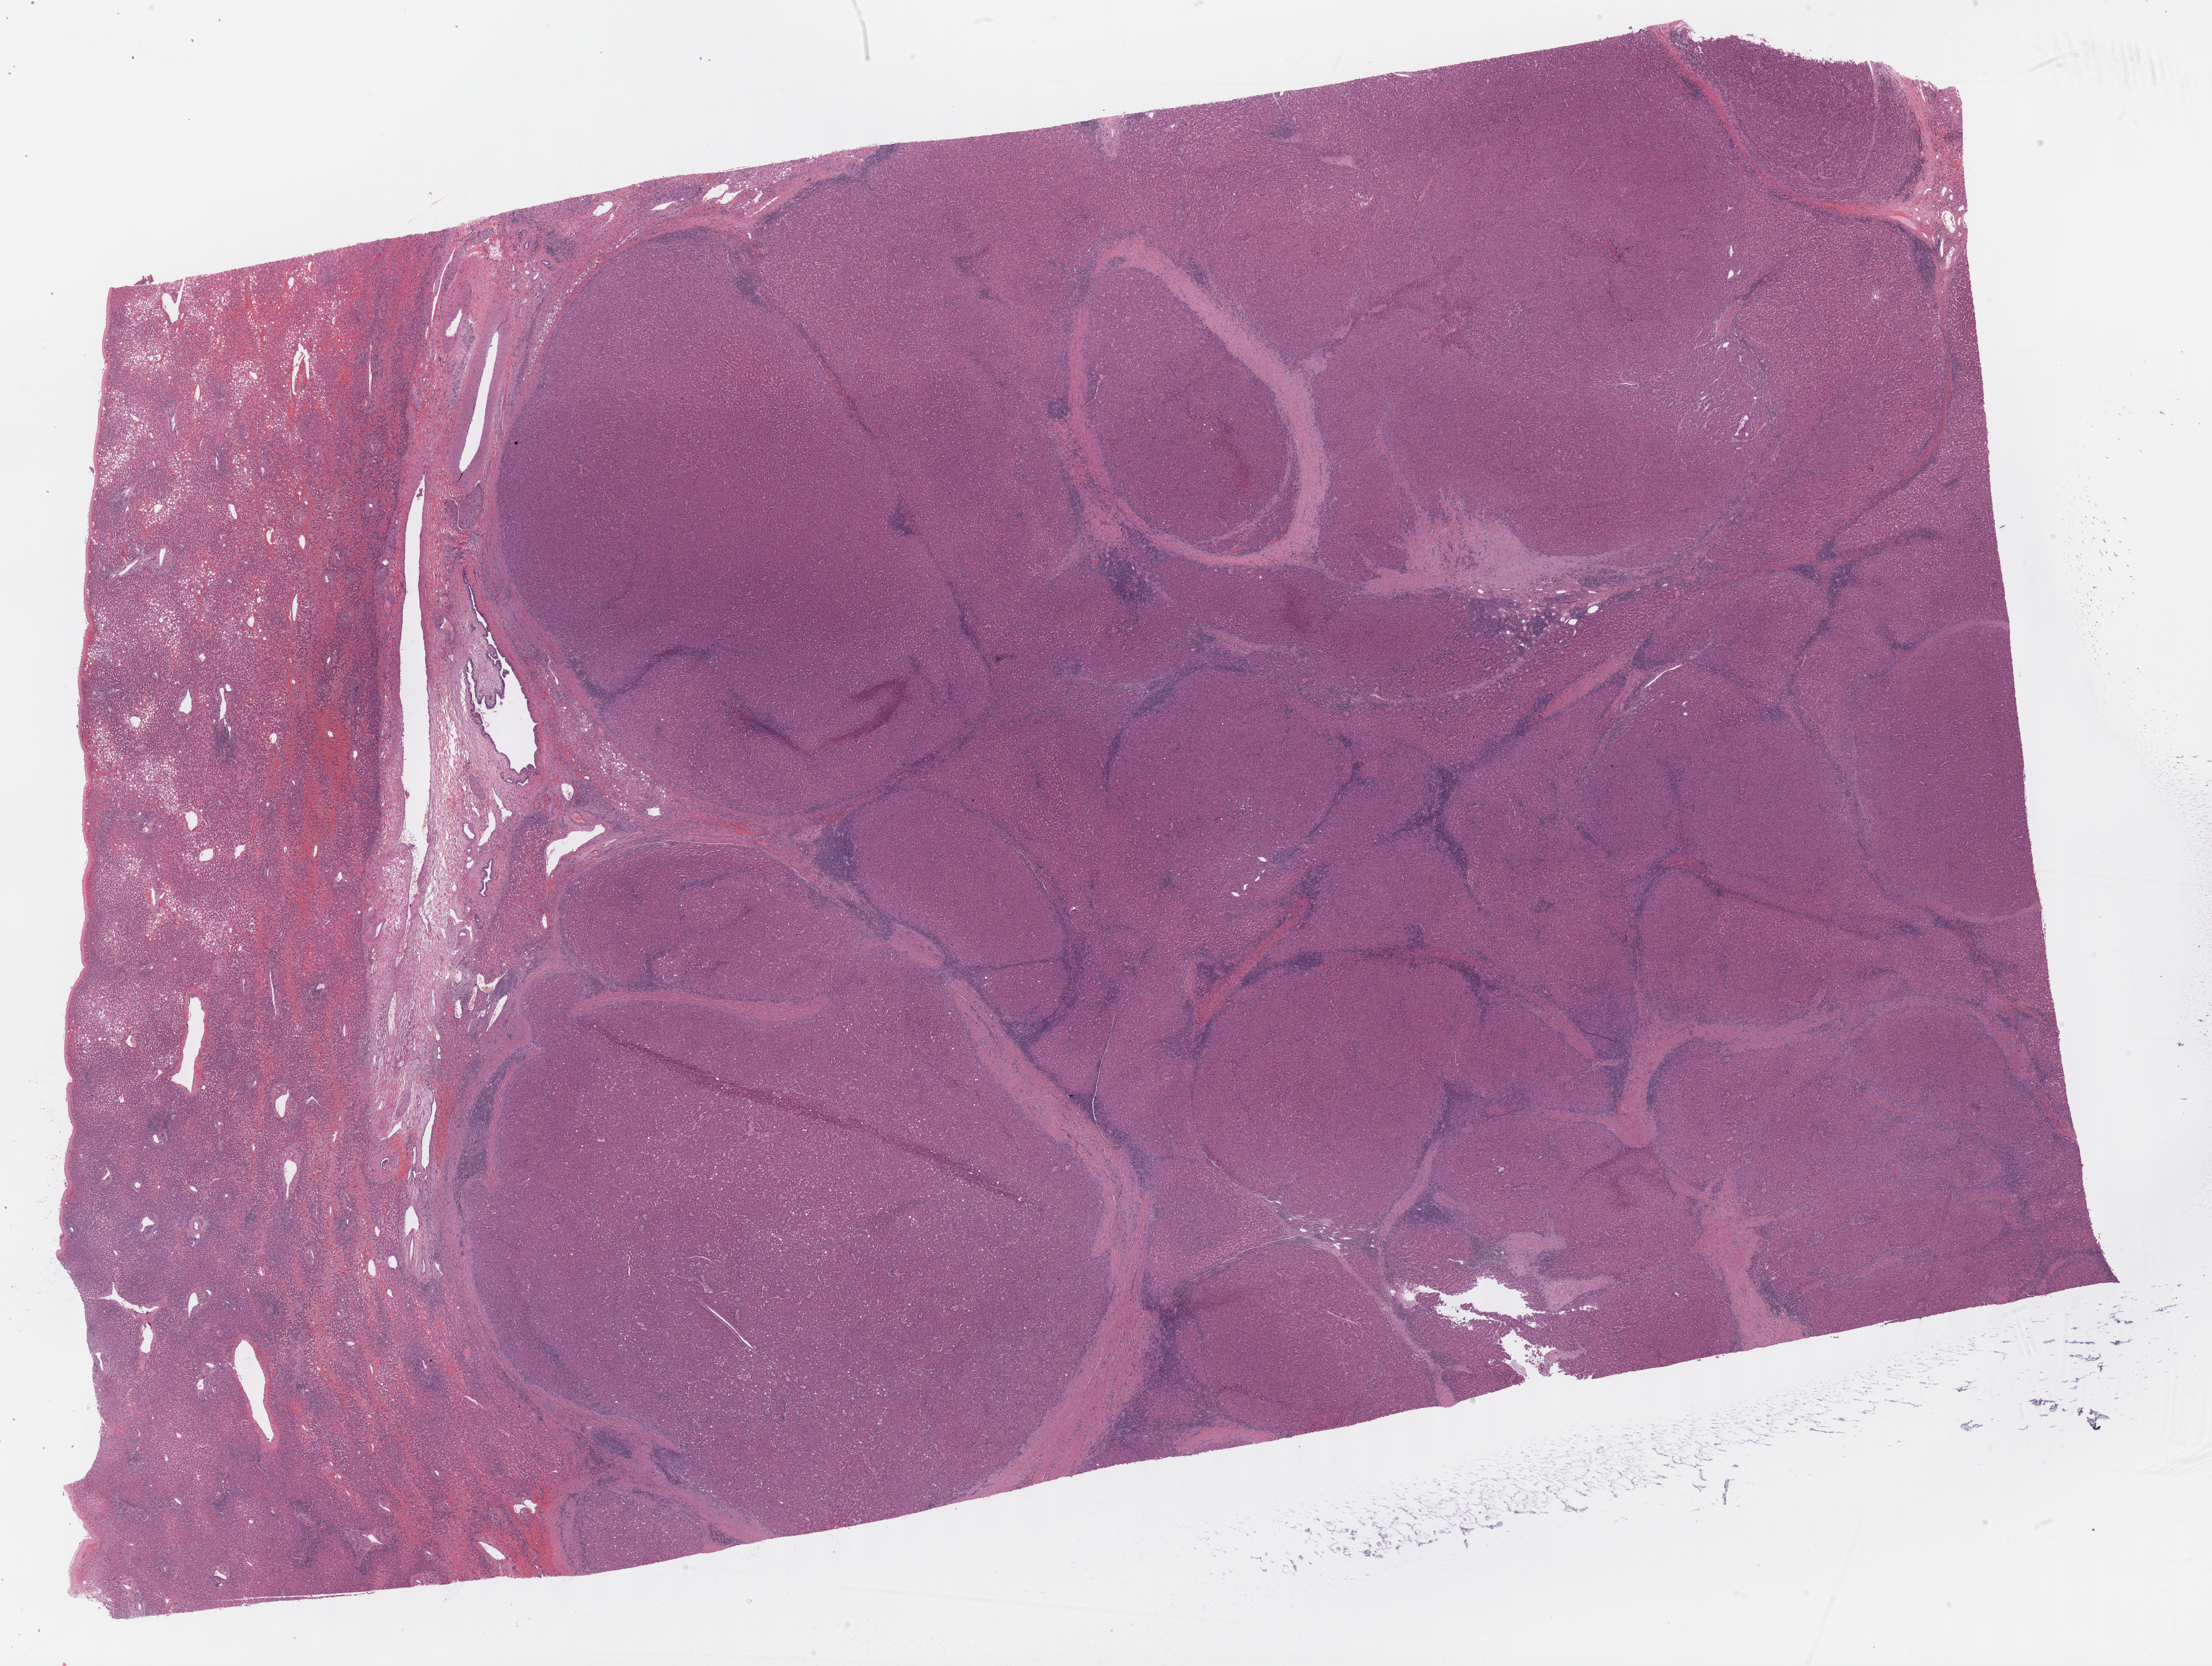
Digitized H&E tissue section (whole slide), a low-resolution overview of the entire scanned area, about 28.7 x 21.6 mm (from a 40x scan). FFPE section. Sample: primary tumour, liver. Male, age 48 years at initial diagnosis. Histologic grade: G2 (moderately differentiated).
* histologic diagnosis: Hepatocellular carcinoma, NOS
* AJCC pathologic stage: I (7th edition)